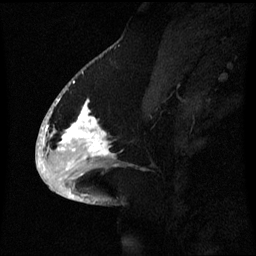
Breast MRI (dynamic contrast-enhanced), one sagittal slice; slice 29 of 60 in the series (ordered by position); dynamic contrast-enhanced series, image 2 of 3 at this slice position (ordered by acquisition); 1.5 T; TE 4.2 ms, TR 8.4 ms; 2.1 mm slice thickness; 256 × 256 image matrix, field of view 220 × 220 mm. Female patient, age 53 years. Case-level facts recorded for this patient, not image findings: setting: breast cancer imaged before/during neoadjuvant chemotherapy; receptor status: HR-positive, HER2-negative.
Structures marked on this image (semi-automatically segmented with operator editing):
- analysis volume of interest (the breast-tissue region the enhancement analysis was run in; not a lesion): bounding box [x1, y1, x2, y2] px = [52, 90, 125, 171]
- tumour enhancement mask (voxels above the 70 % enhancement threshold inside the analysis volume of interest): [55, 100, 111, 159]